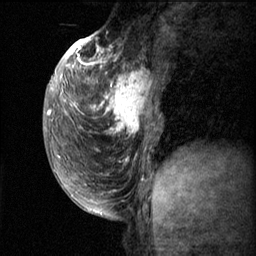
Breast MRI (dynamic contrast-enhanced), one sagittal slice; position 23 of 60 along the scan axis; dynamic contrast-enhanced series, image 2 of 3 at this slice position (ordered by acquisition); 1.5 T; TE 4.2 ms, TR 11.1 ms; 256 × 256 image matrix, field of view 180 × 180 mm. Patient: female, 50 years.
Outlined on this slice (semi-automatically segmented with operator editing):
- analysis volume of interest (the breast-tissue region the enhancement analysis was run in; not a lesion): box from (x=82, y=56) to (x=165, y=143) px
- tumour enhancement mask (voxels above the 70 % enhancement threshold inside the analysis volume of interest): (x=82, y=56)–(x=152, y=135)